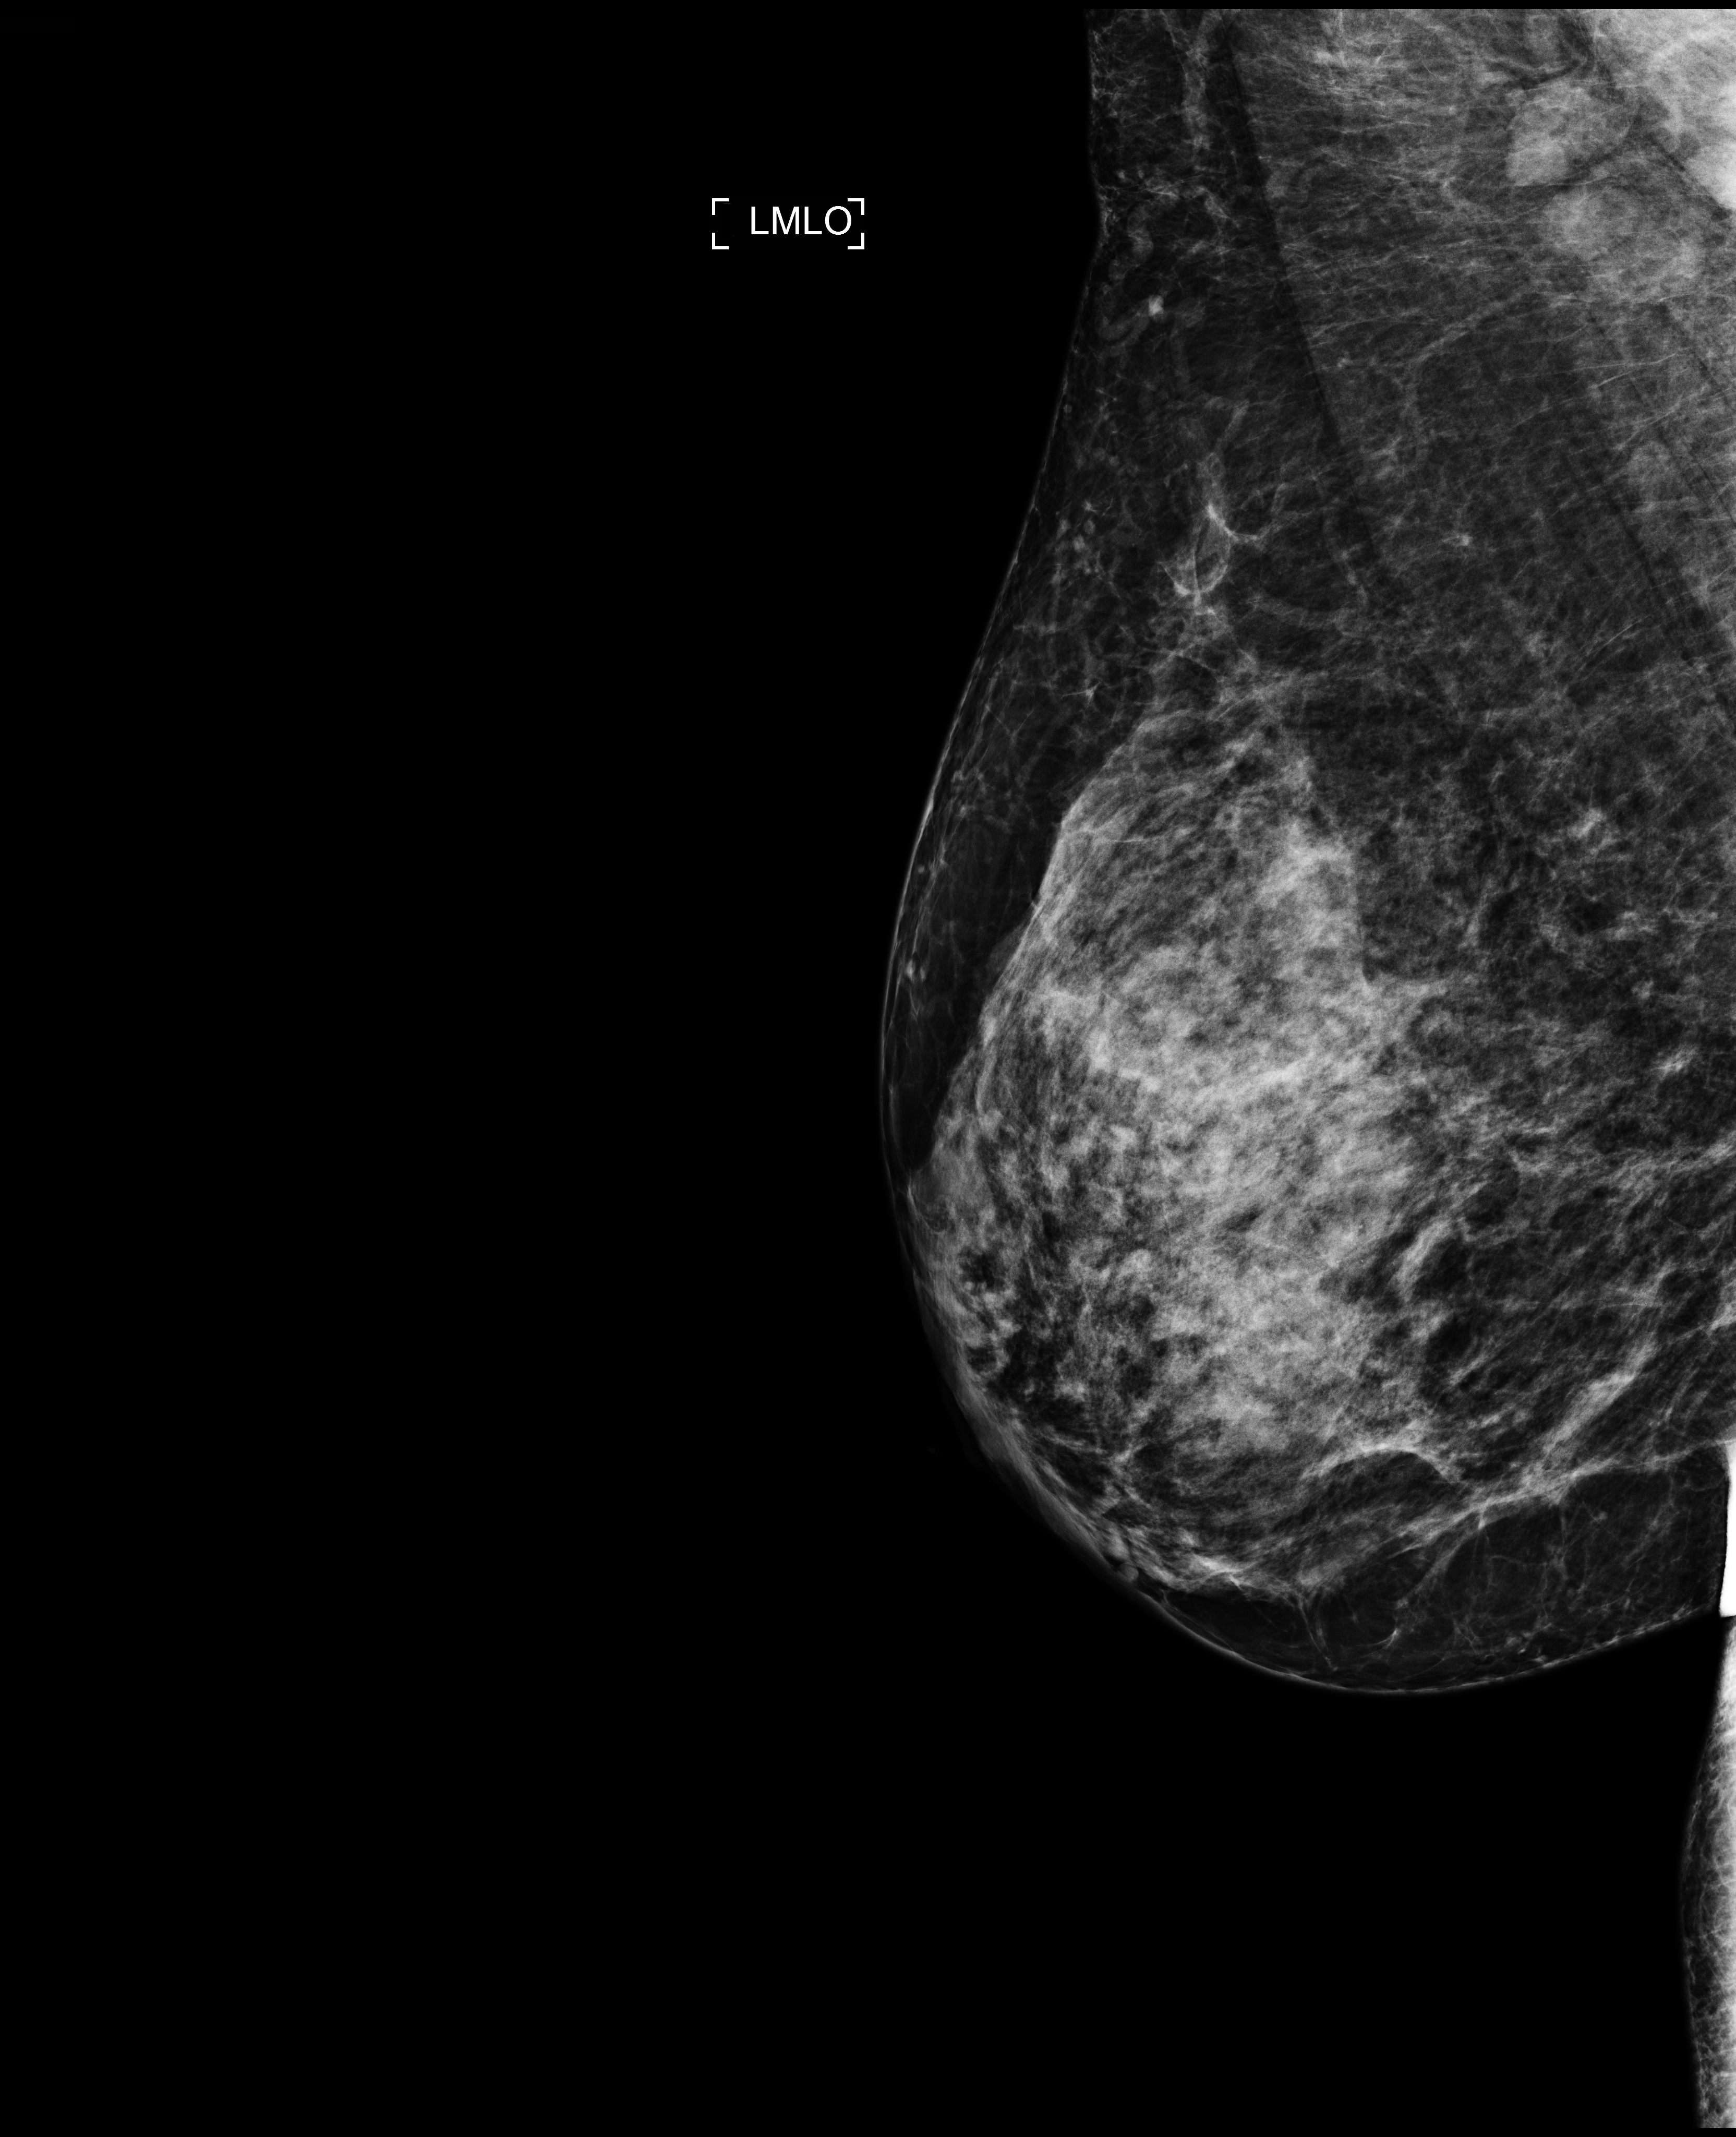
Annual screening mammography examination, compressed breast thickness 81 mm, system: Selenia Dimensions. Patient: female, 43 years.
Image type: full-field digital mammogram. Breast: left. Projection: medio-lateral oblique projection.